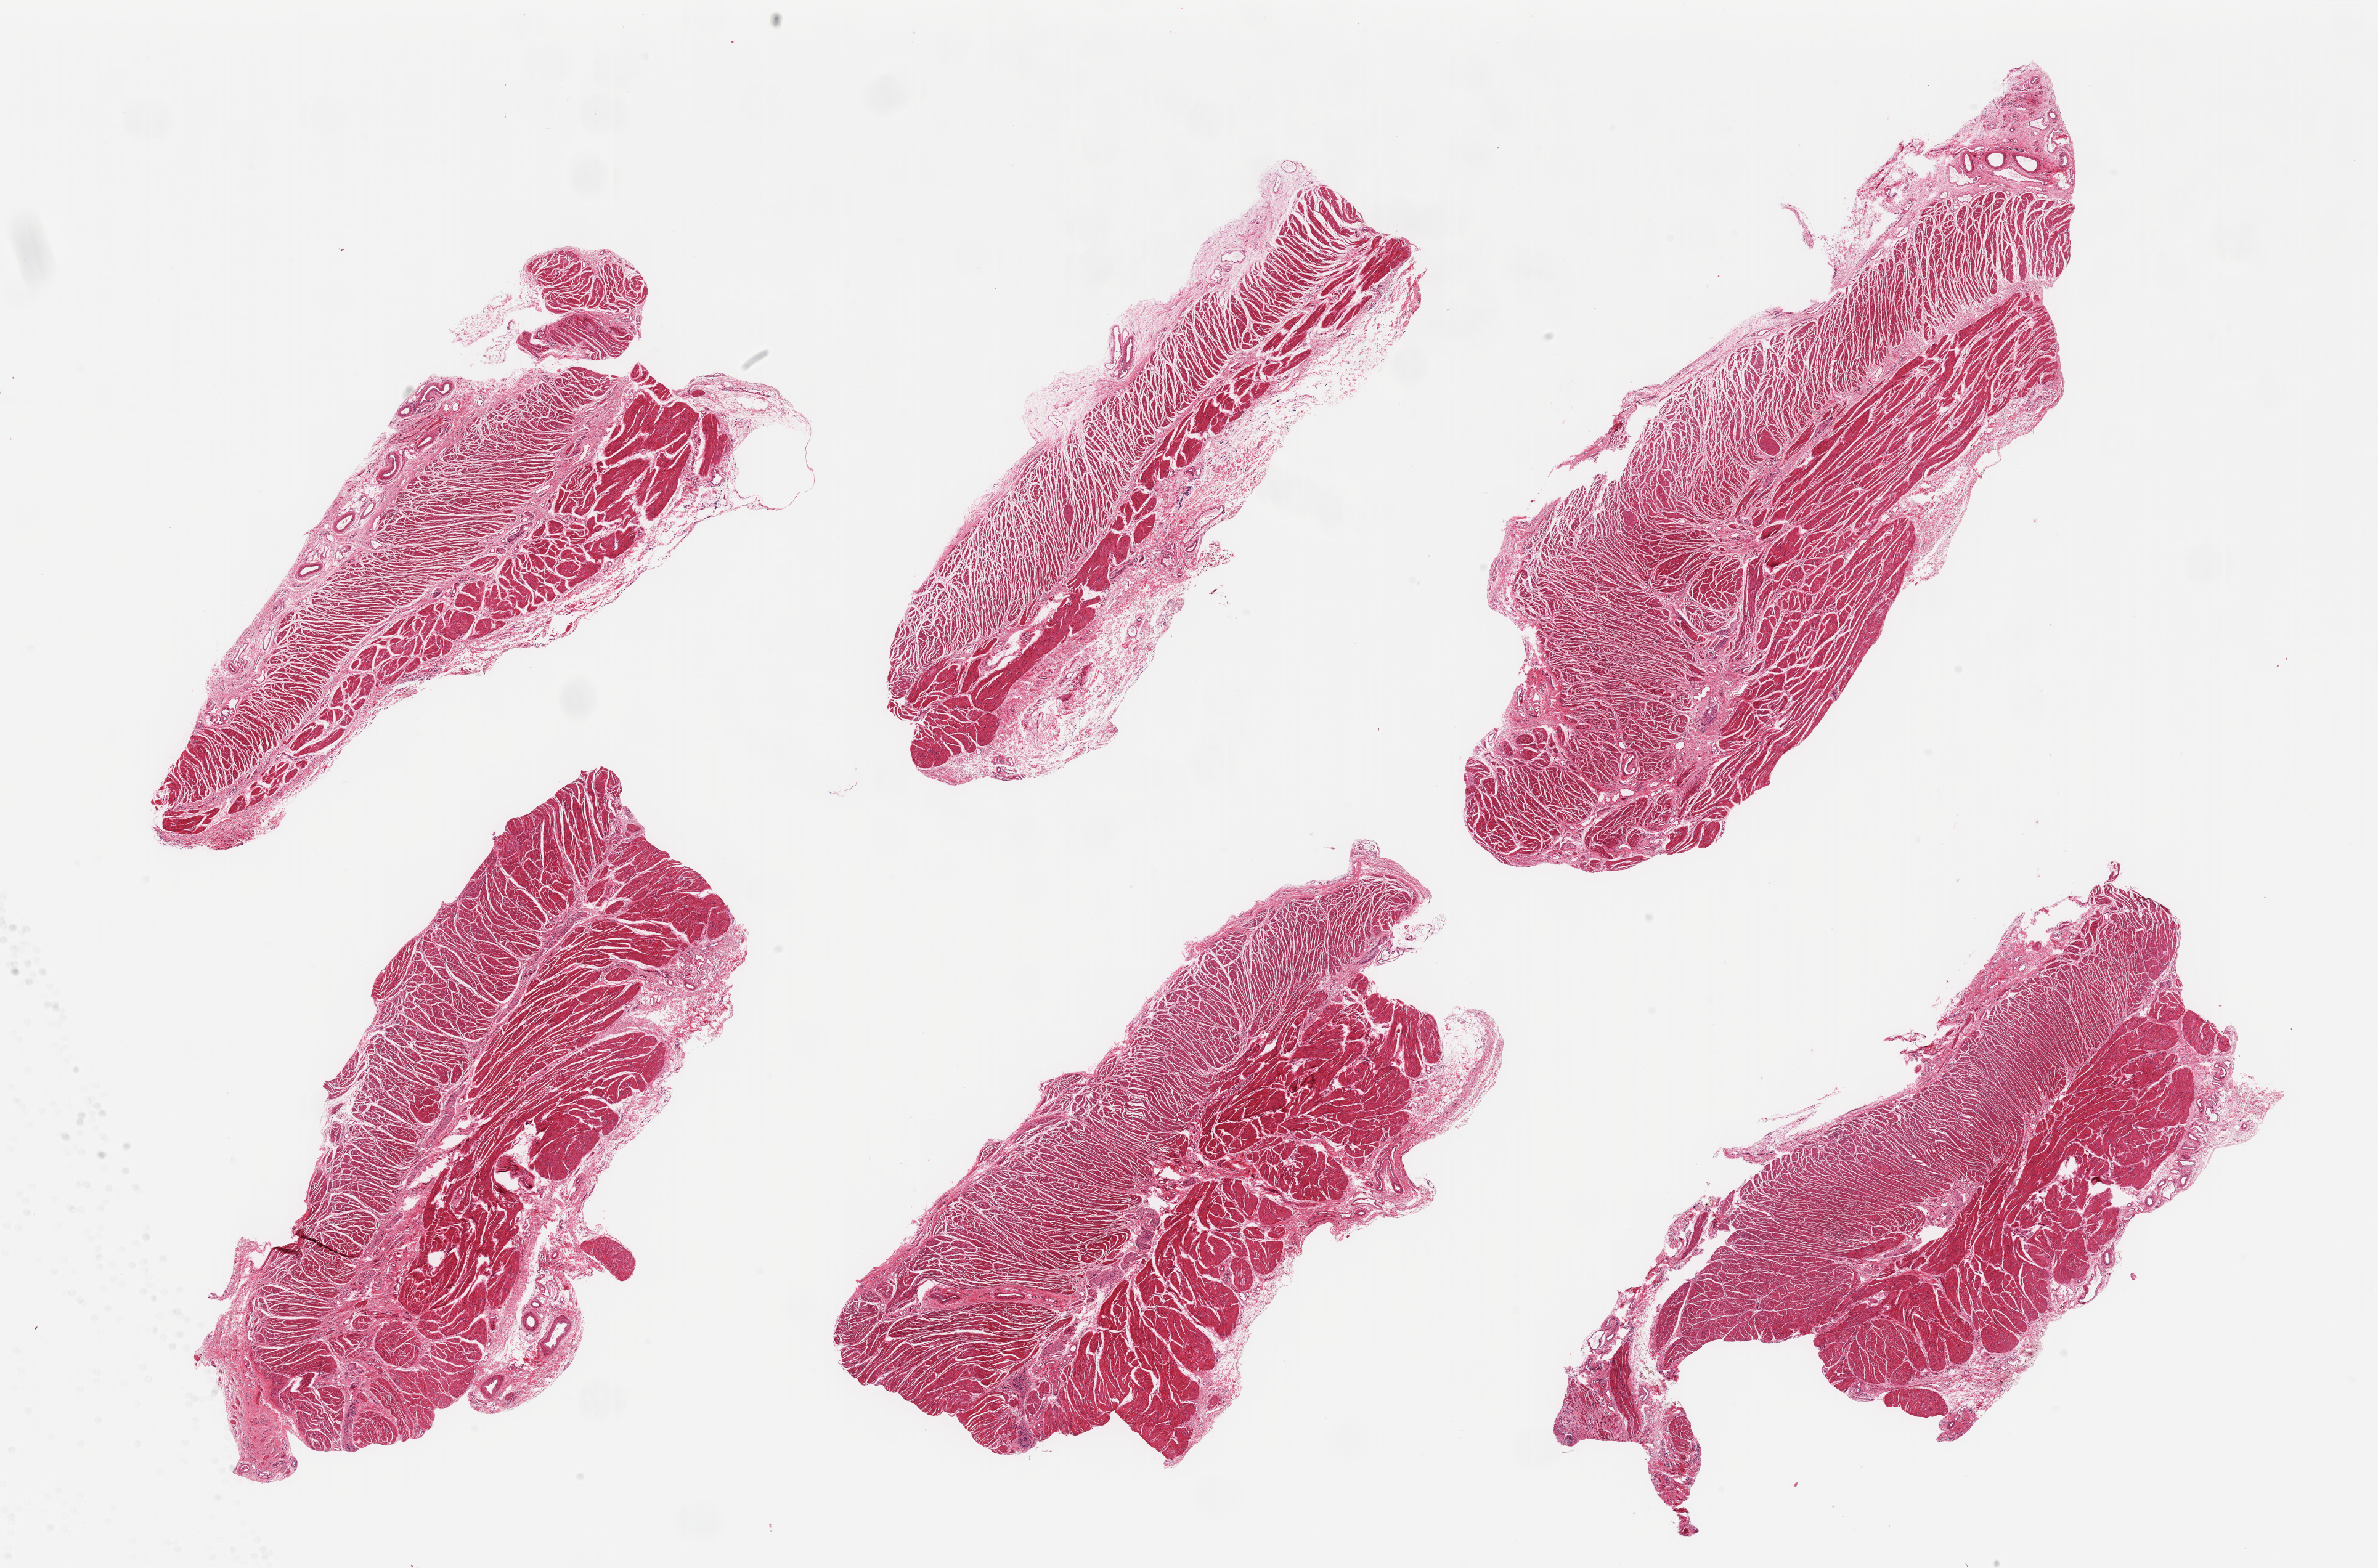
Hematoxylin and eosin (H&E) whole-slide image, low-resolution overview of the scanned area, about 30.5 x 20.1 mm; PAXgene-fixed, paraffin-embedded tissue; target tissue: gastroesophageal junction; donor tissue sample. Donor sex: female.
Pathologist's review note for this sample: 6 pieces; target muscularis, some residual attached submucosa/vessels.